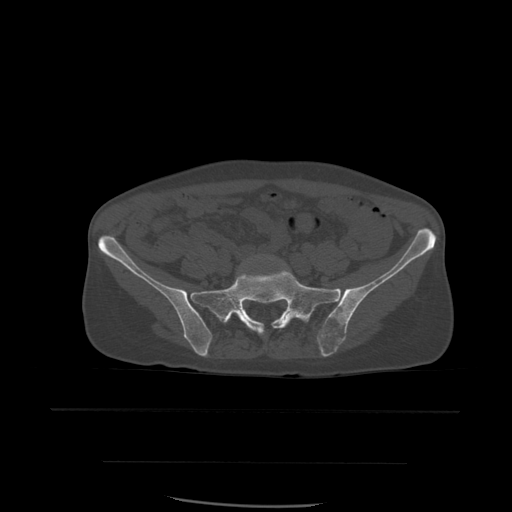
CT including the spine, one axial slice; slice 130 of 574 in the series (ordered by position); bone window (W 1800 / L 400 HU); 1.25 mm slice thickness; 512 × 512 image matrix, field of view 392 × 392 mm. Patient age 48 years. Case-level facts recorded for this patient, not image findings: primary cancer: lung; vertebrae with lytic lesions (as recorded): T11.
Annotated regions visible in this slice (semi-automatically segmented with operator editing):
- L5 vertebra: box from (x=258, y=257) to (x=302, y=319) px